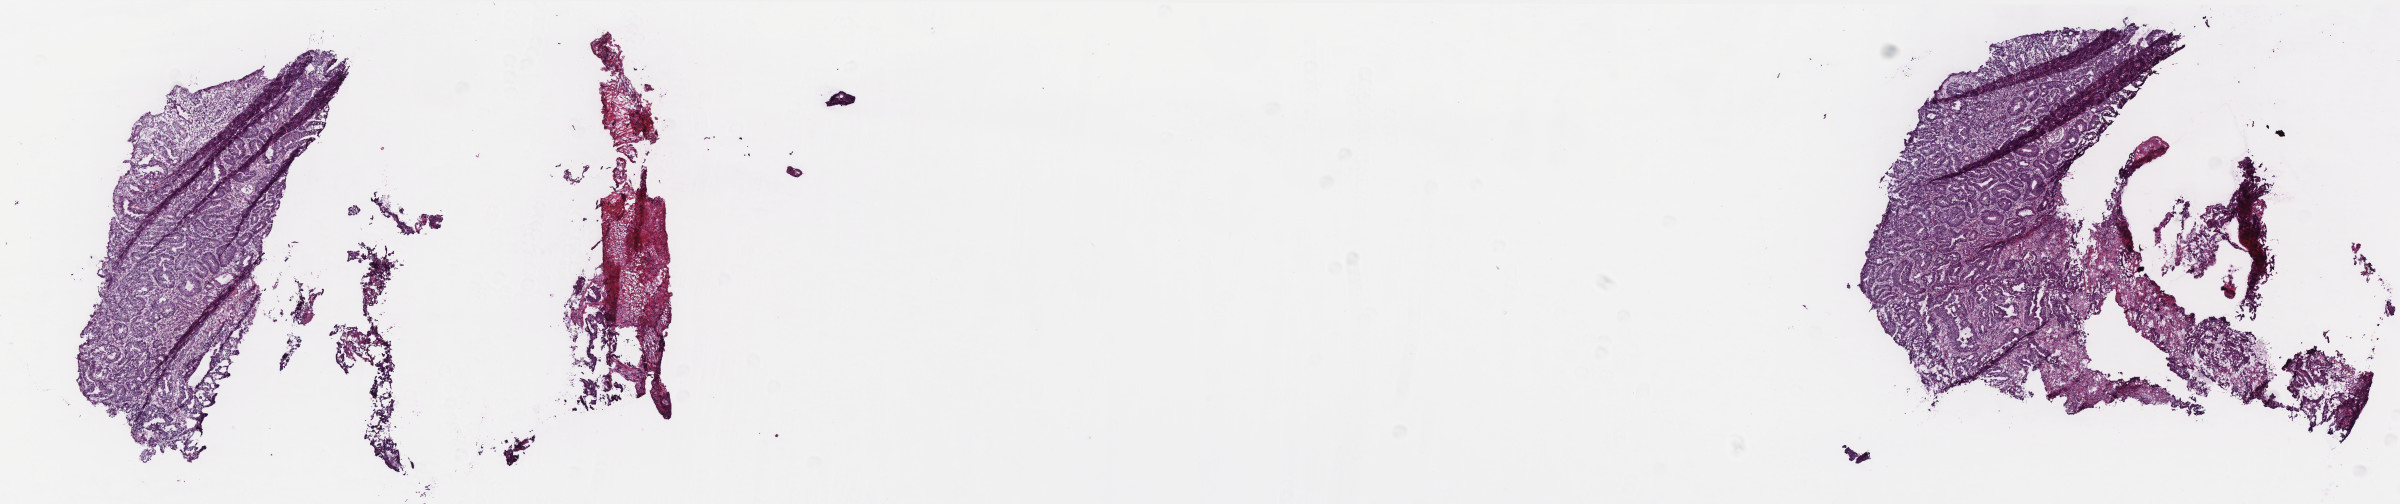
Whole-slide histology image, Hematoxylin and eosin (H&E) stained — whole scanned area (about 19.2 x 4.0 mm, acquisition: 40x scan) shown as a low-resolution overview, frozen section from the top of the tissue portion, colon, primary tumour sample. Male, age 75 years at initial diagnosis. Pathologist review of this section (percent, as recorded): tumour cells 95%, tumour nuclei 90%.
Histologic diagnosis: Adenocarcinoma, NOS (ascending colon).